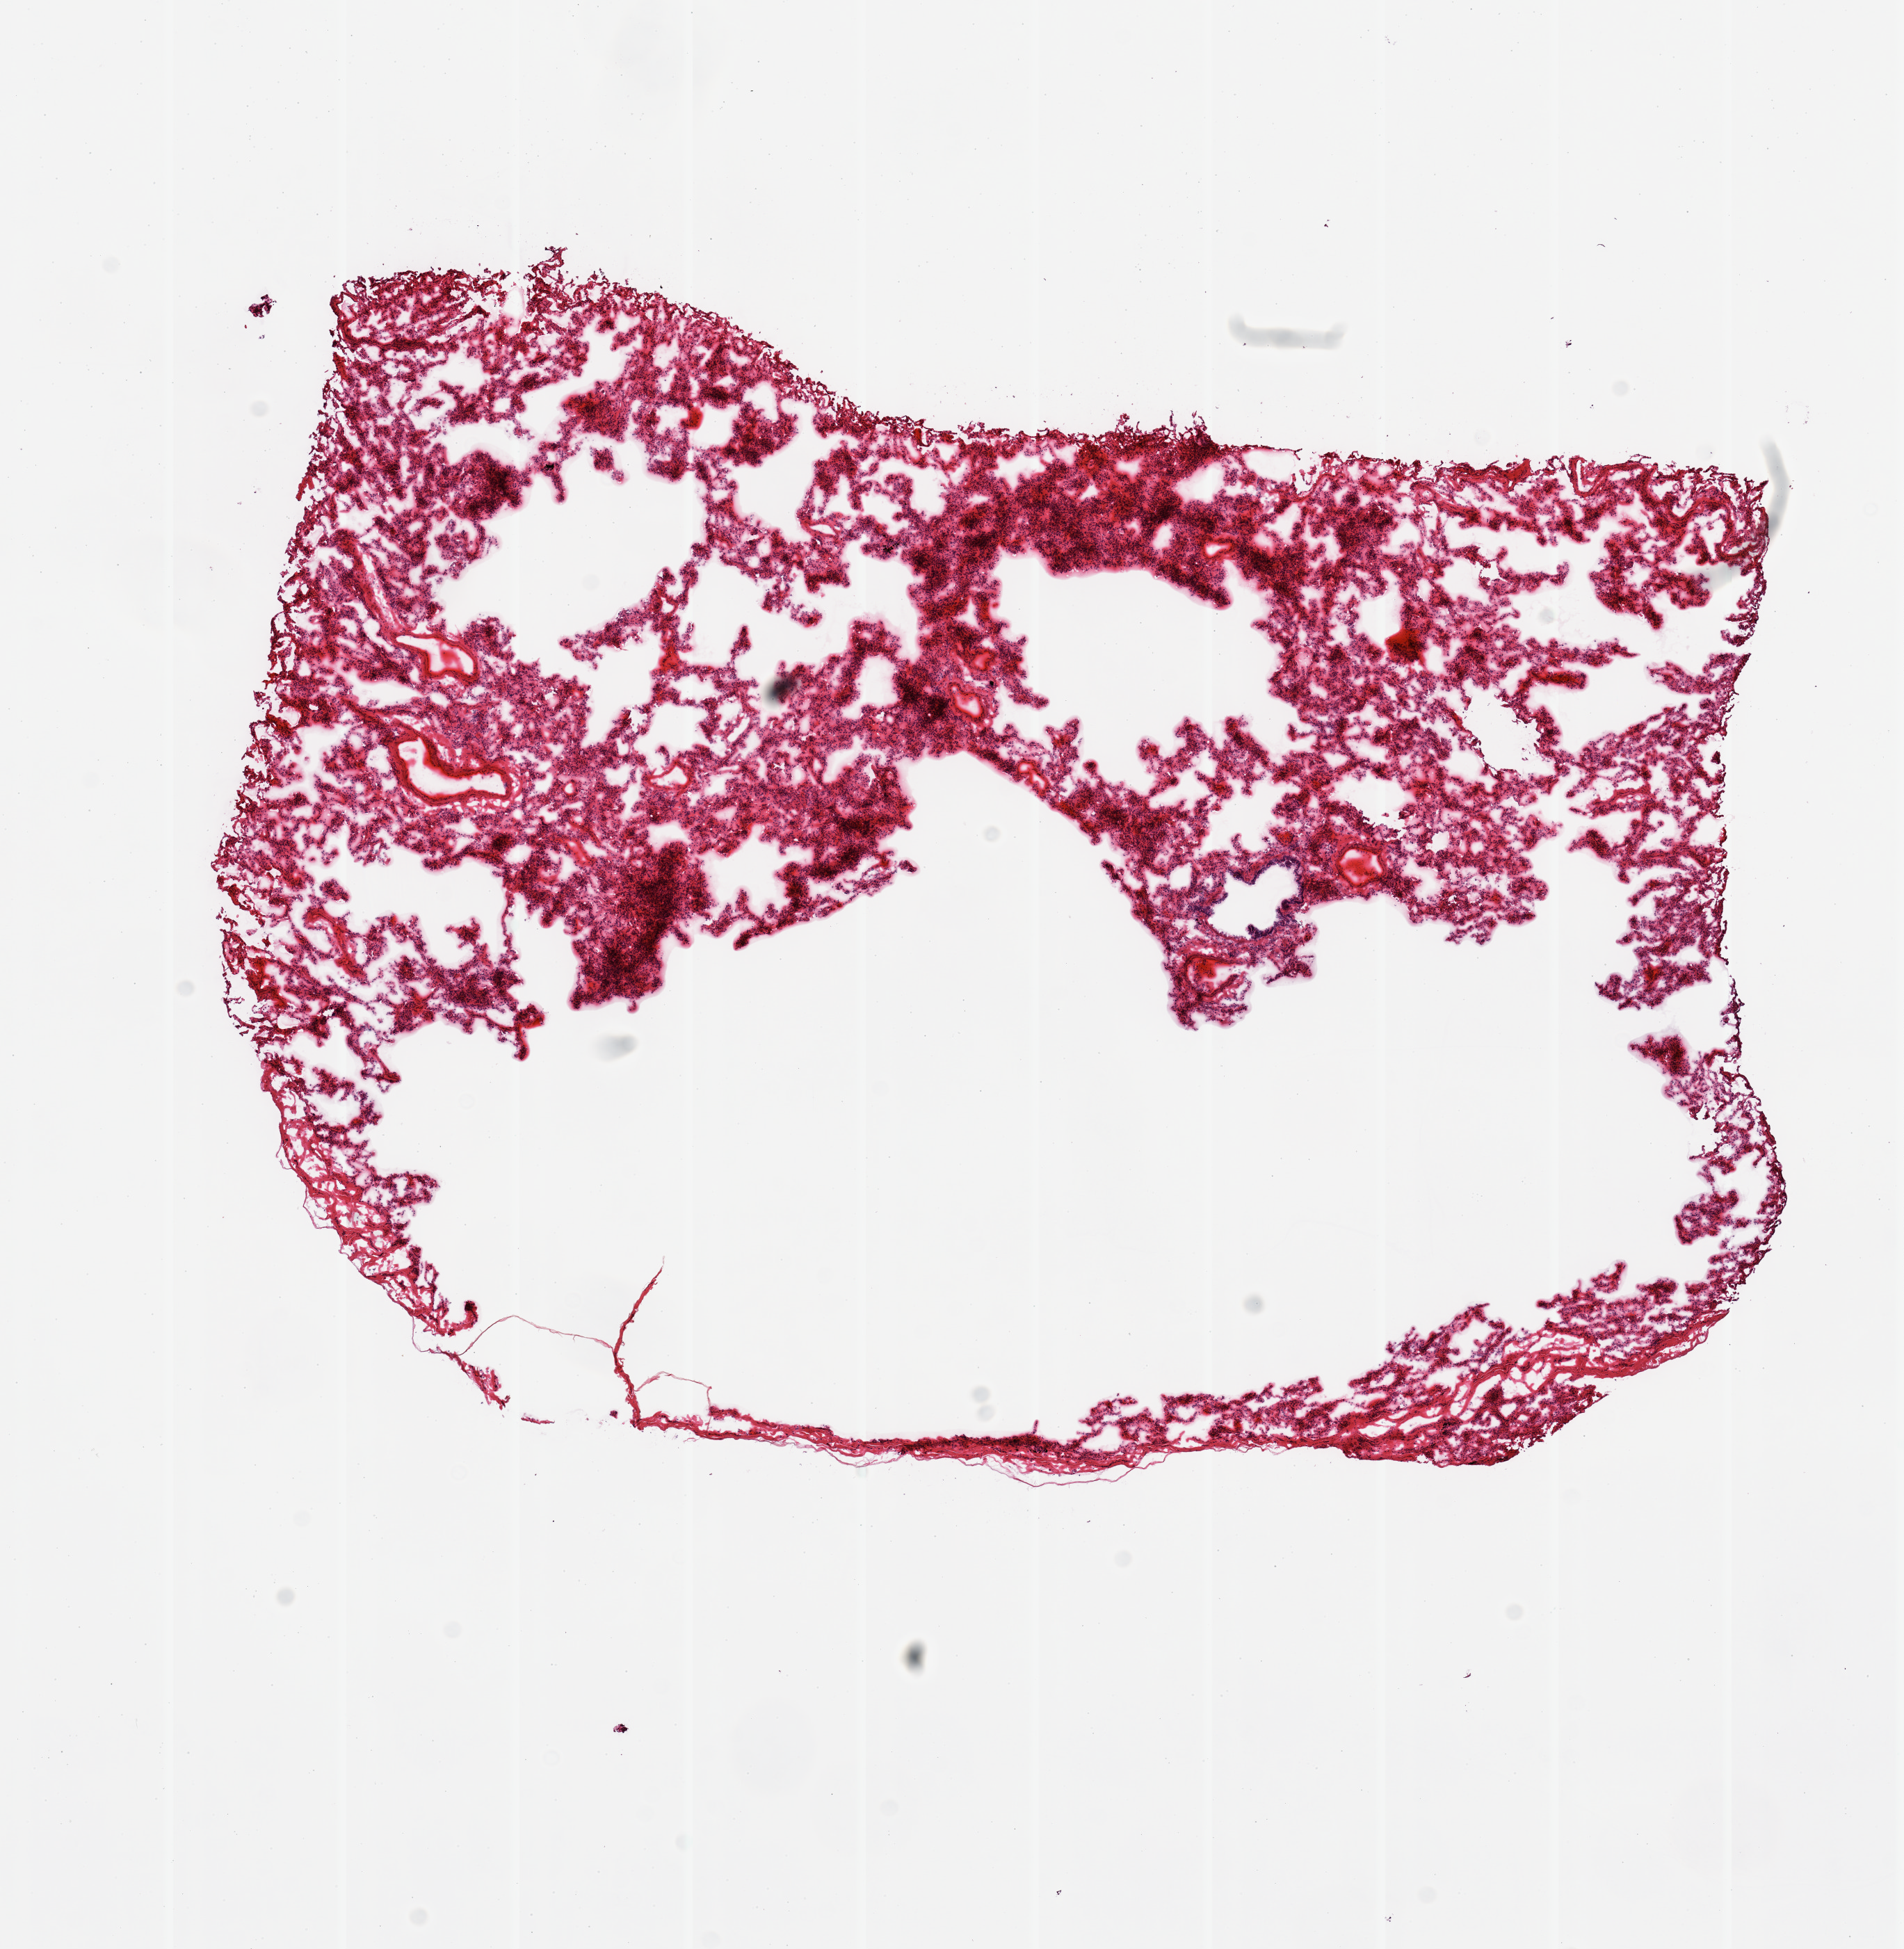
Digitized haematoxylin and eosin-stained section, shown as a low-resolution overview of the whole scanned area (about 10.8 x 11.1 mm). Female donor.
Specimen: frozen section (dry ice); section of lung (target tissue); donor tissue sample.